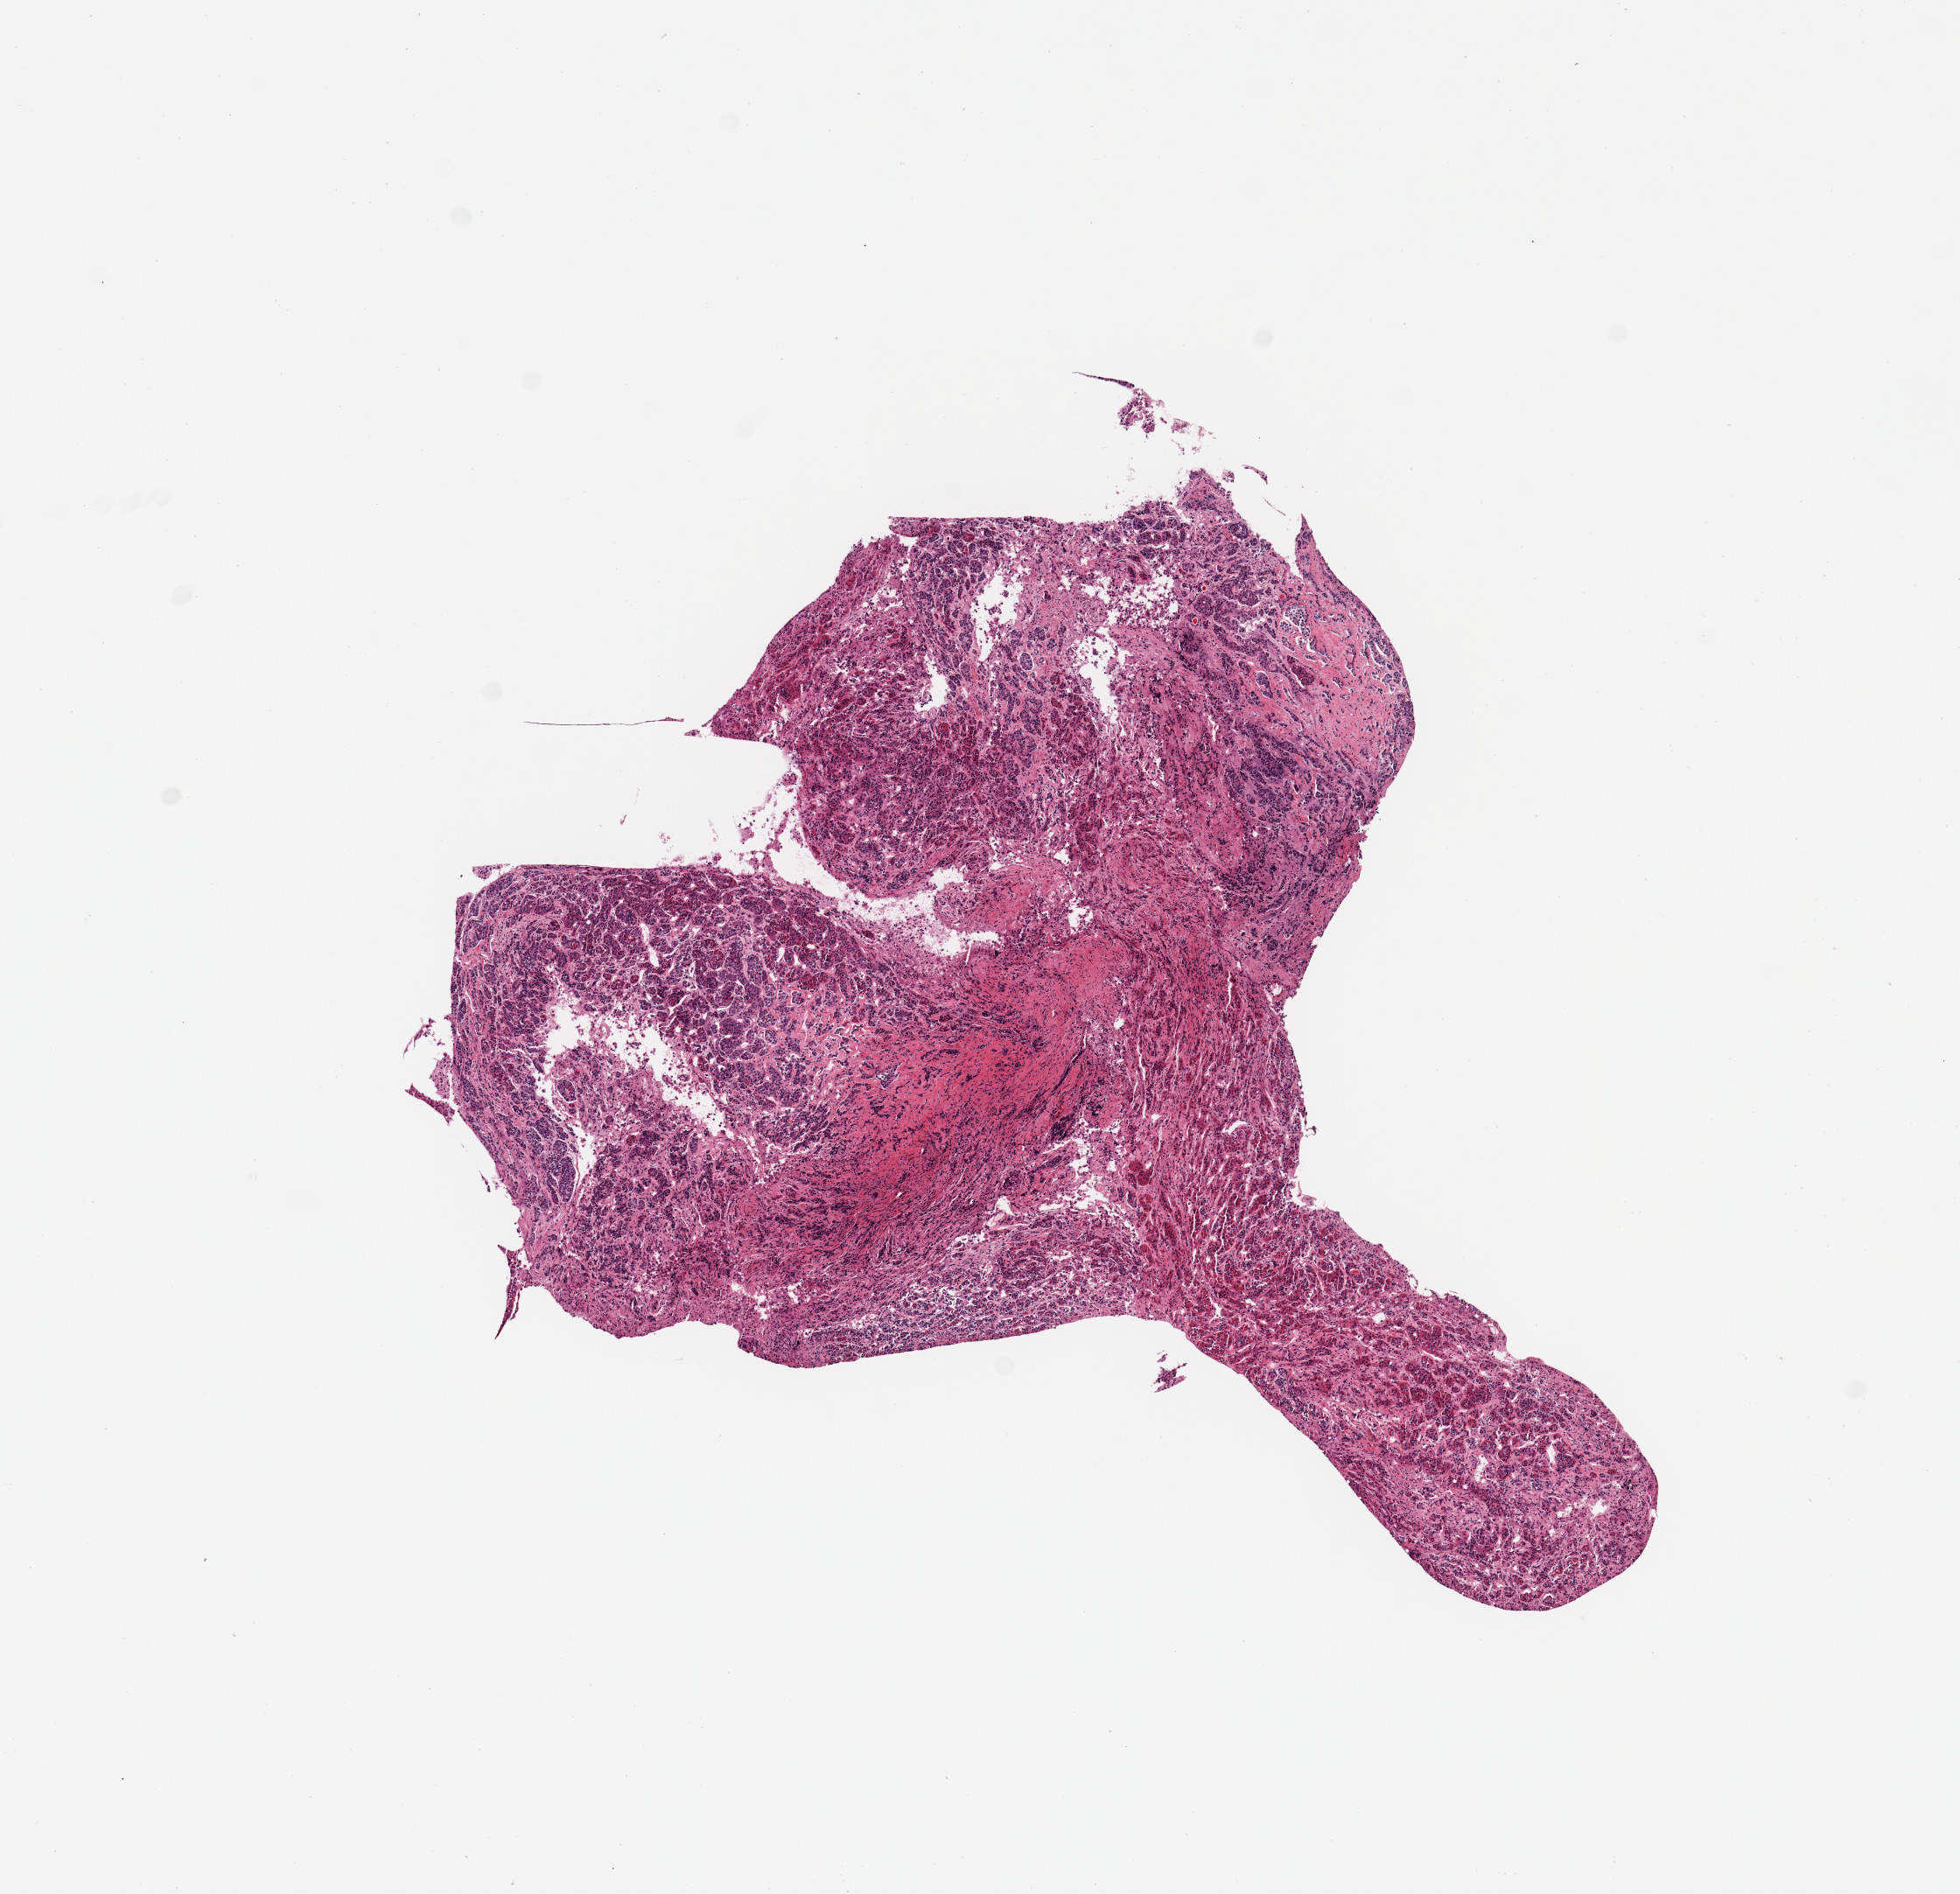
Hematoxylin and eosin (H&E) whole-slide image, shown as a low-resolution overview of the whole scanned area (about 8.9 x 8.6 mm); PAXgene-fixed paraffin-embedded (PFPE) section; target tissue: pituitary; tissue donor sample. Donor: male.
Review note (as recorded): 1 piece of partly fragmented adenohypophysis.